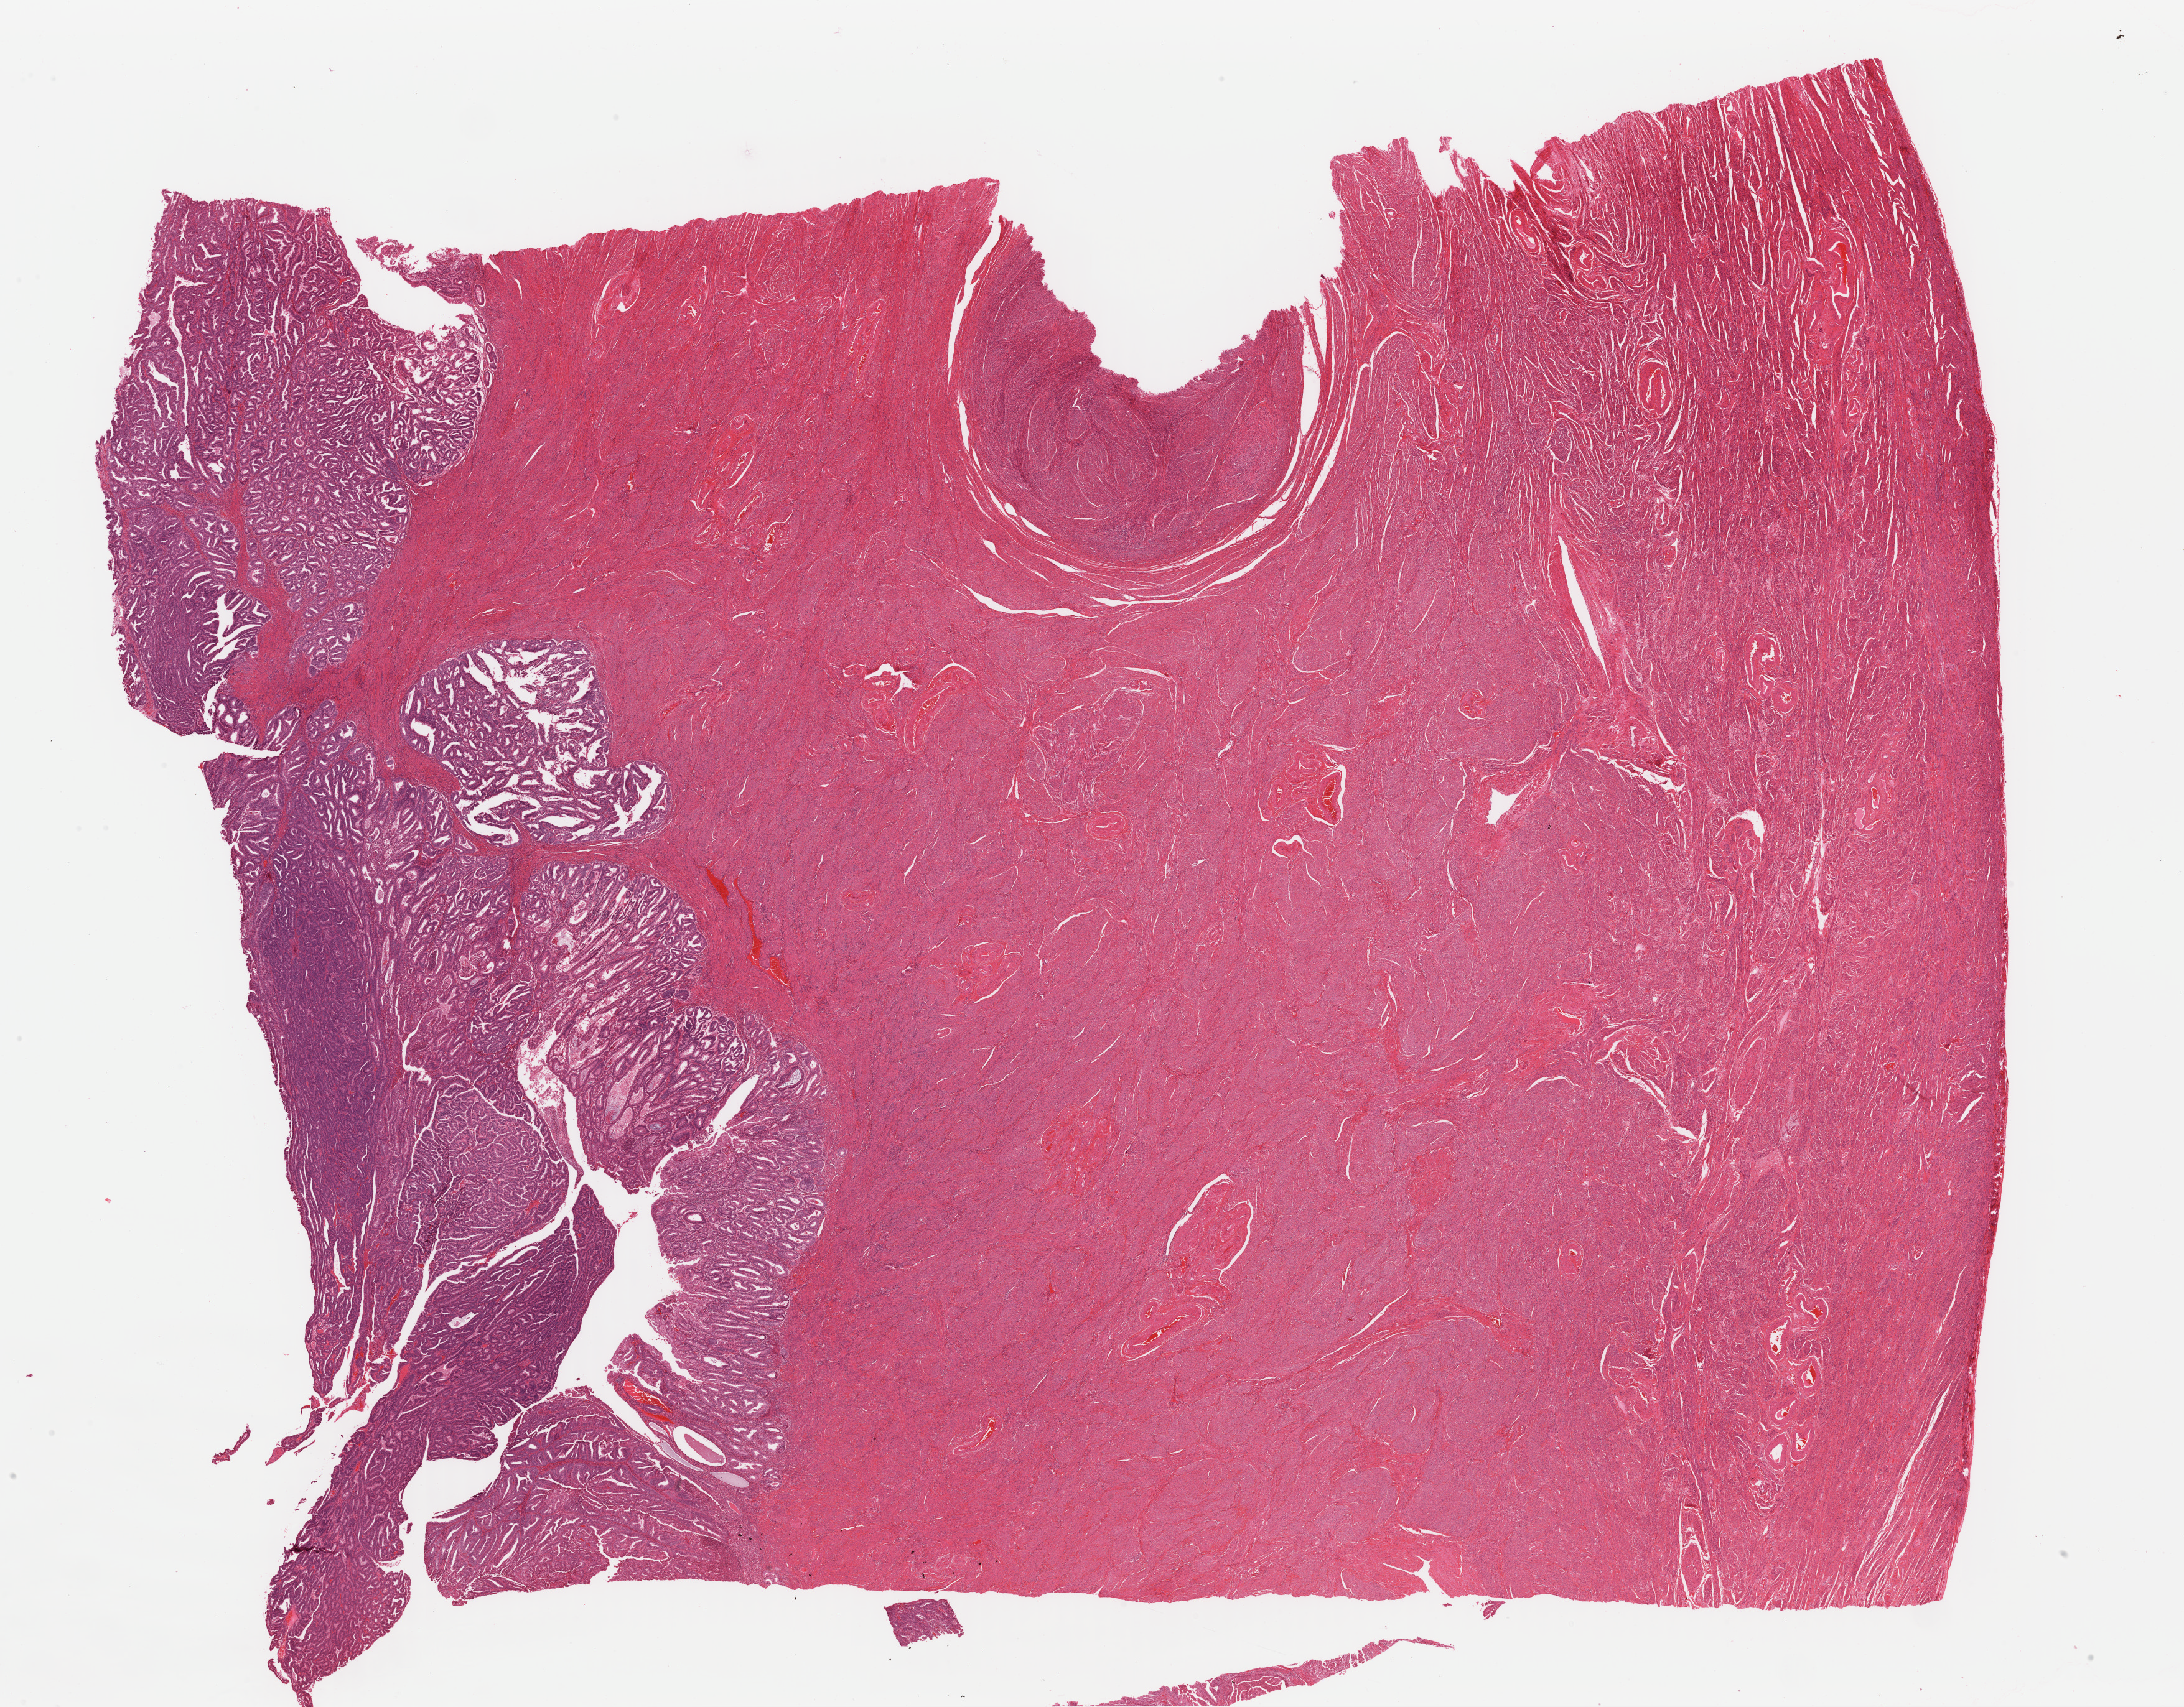
Digitized Hematoxylin and eosin (H&E) stained tissue section (whole slide), low-resolution overview of the scanned area, about 27.7 x 21.7 mm. FFPE section. Primary tumour sample from the uterus. Female patient; age at initial diagnosis 57 years. Histologic grade: G1 (well differentiated).
Lymph nodes positive (case pathology): 0 of 24 examined. Histologic diagnosis: Endometrioid adenocarcinoma, NOS (endometrium). FIGO stage: IB.